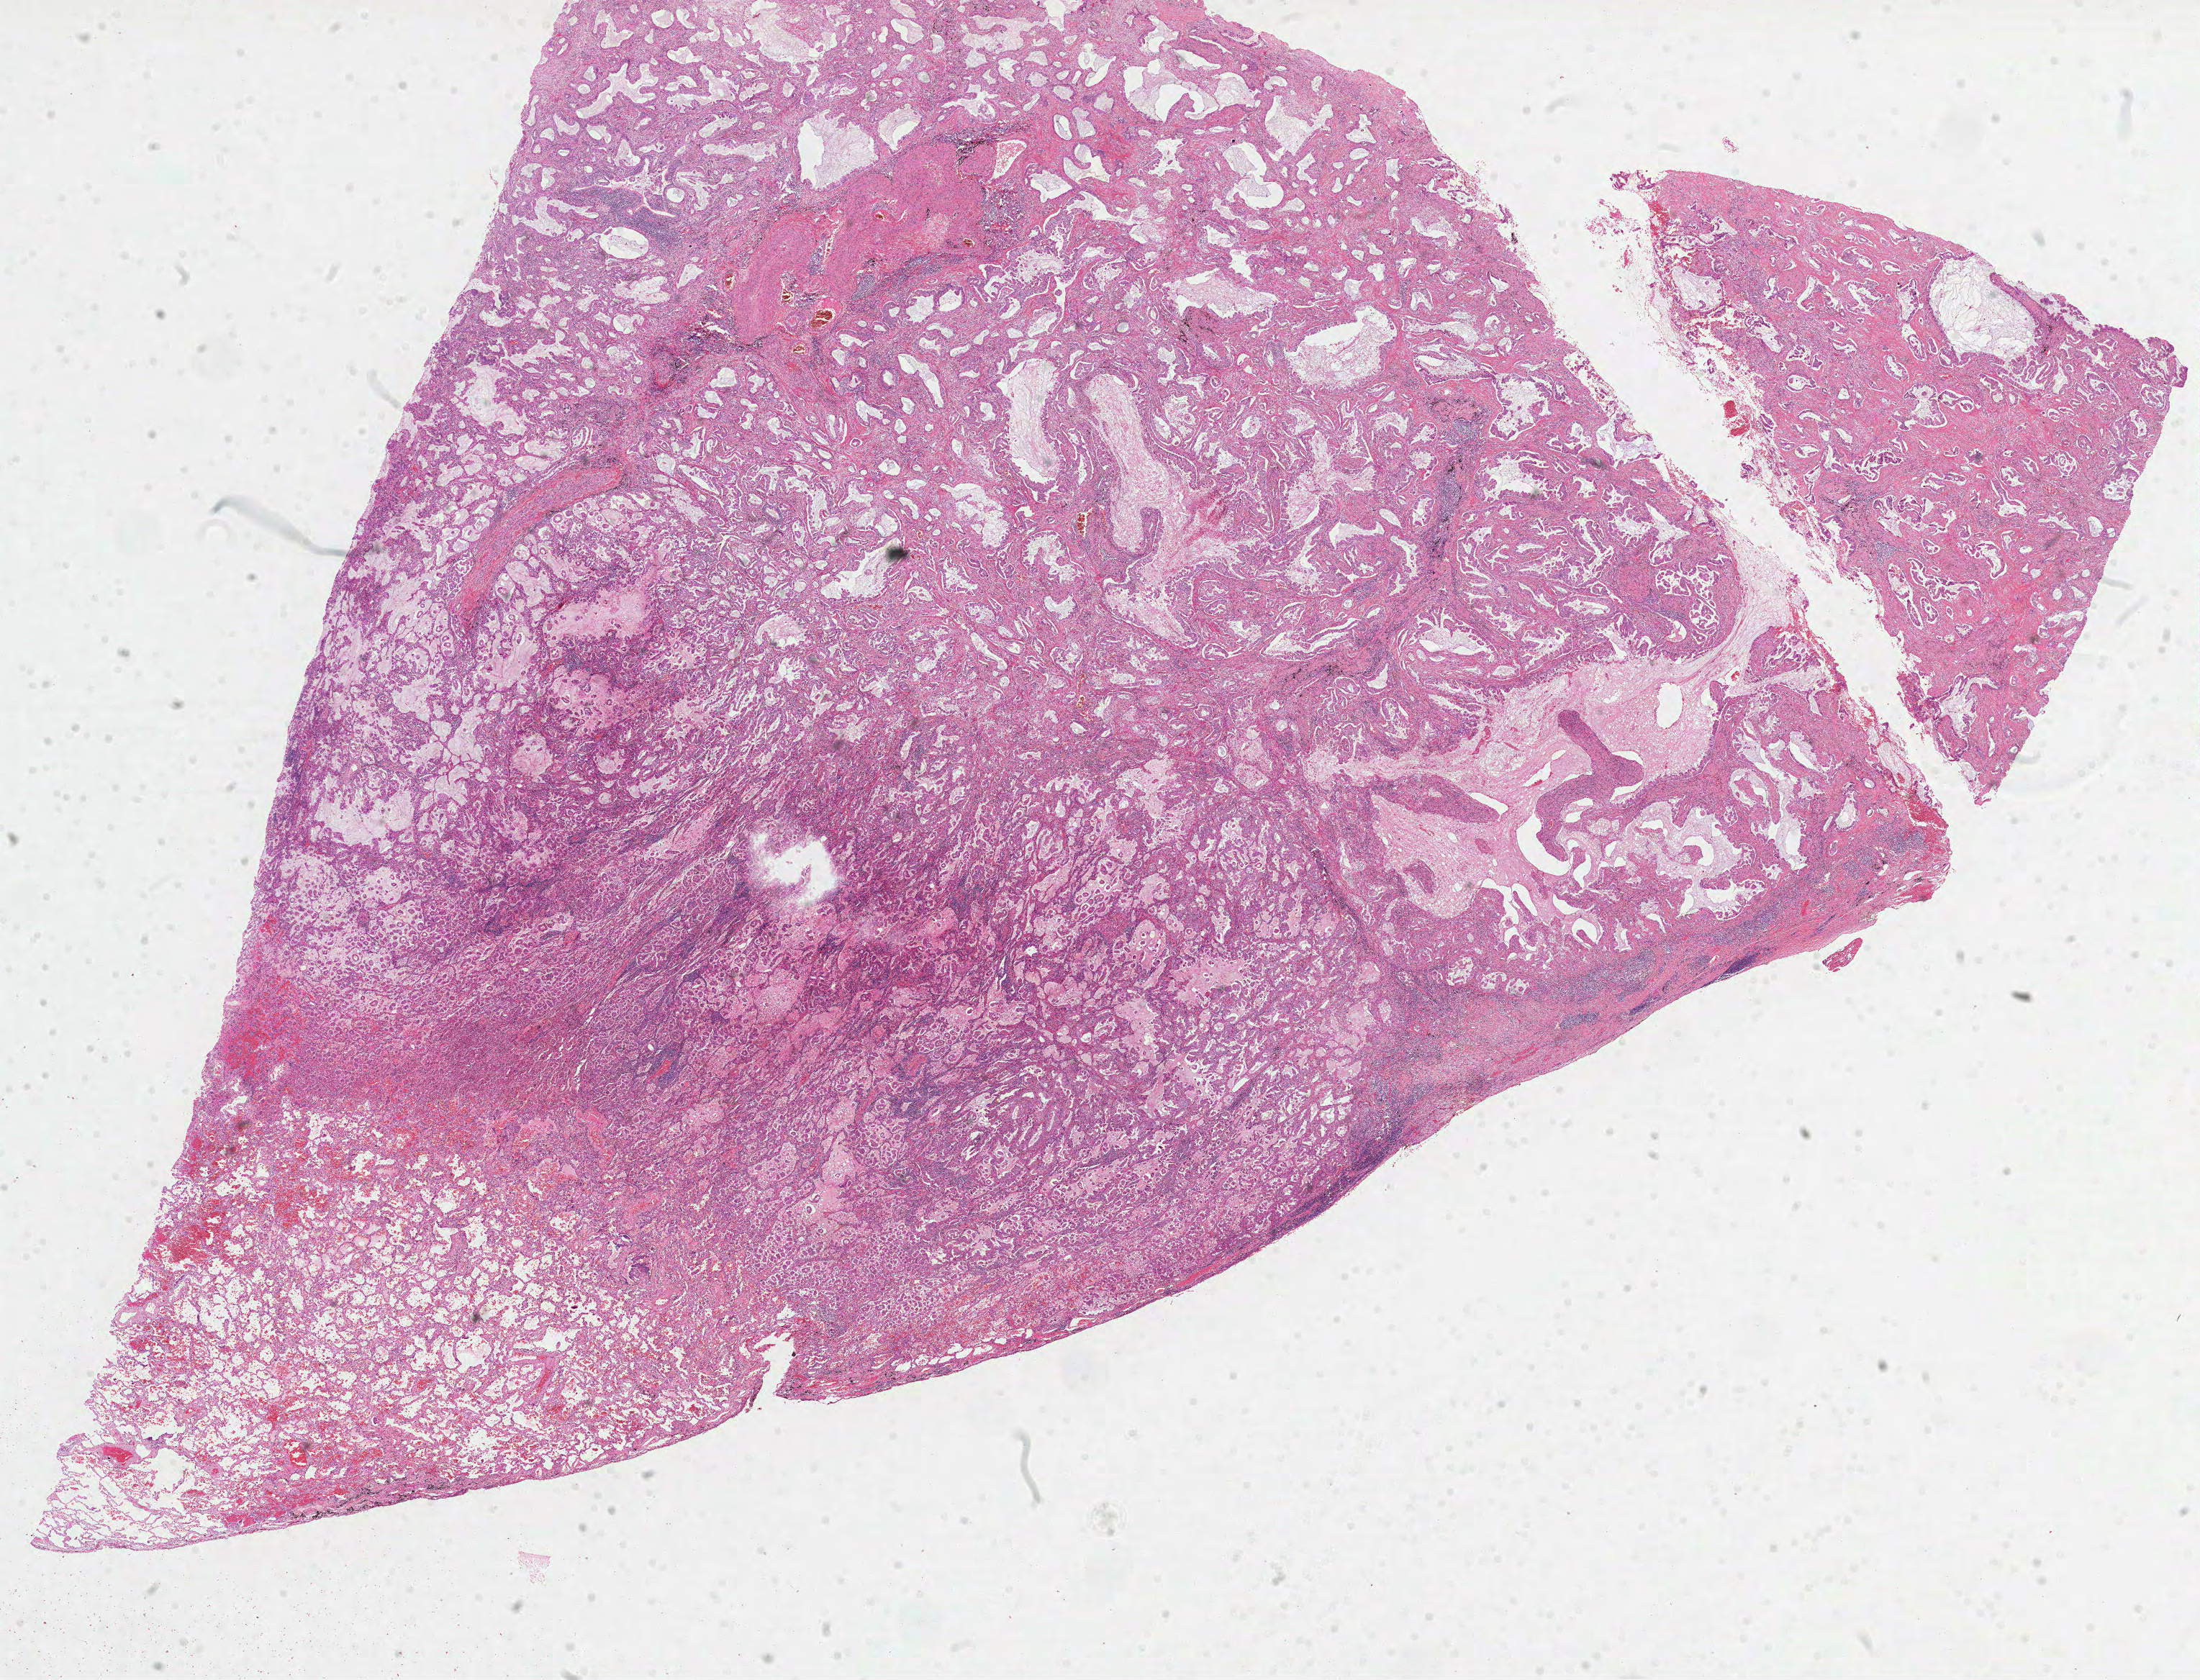
H&E-stained whole-slide image — a low-resolution overview of the entire scanned area, about 24.7 x 18.8 mm (slide scanned at 40x); formalin-fixed paraffin-embedded (FFPE) diagnostic section; sample: primary tumour, lung. Male patient; age at initial diagnosis 61 years.
AJCC pathologic stage: IV. Laterality: right. Pathologic diagnosis: Adenocarcinoma with mixed subtypes (lower lobe, lung).